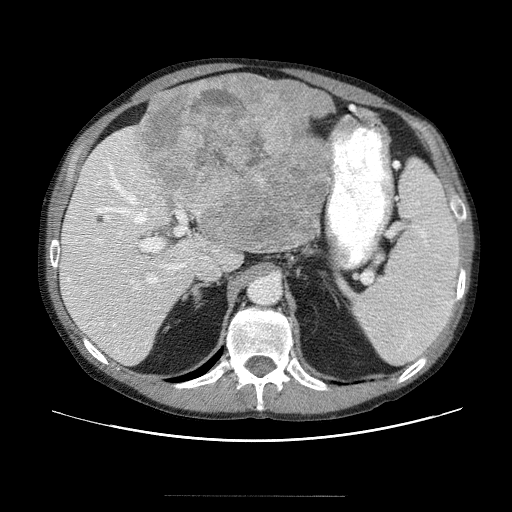
Contrast-enhanced abdominal CT (liver protocol), one axial slice; position 31 of 69 along the scan axis; reconstruction kernel STANDARD; 120 kVp; soft-tissue window (W 400 / L 40 HU); 512 × 512 image matrix. Case-level facts recorded for this patient, not image findings: diagnosis: hepatocellular carcinoma (patient treated with transarterial chemoembolisation; whether this scan precedes or follows treatment is not stated here); TNM stage (as recorded): Stage-IVB; Child-Pugh class: B; tumour differentiation: poorly differentiated; tumour nodularity: multinodular.
Annotated regions visible in this slice (semi-automatic segmentation, software-assisted and operator-edited):
- liver parenchyma outside the tumour (the mass and vessels are separate outlines, so this box may not span the whole liver): bounding box [x1, y1, x2, y2] px = [58, 90, 330, 364]
- mass: [134, 74, 335, 257]
- liver vessels: [68, 148, 238, 343]